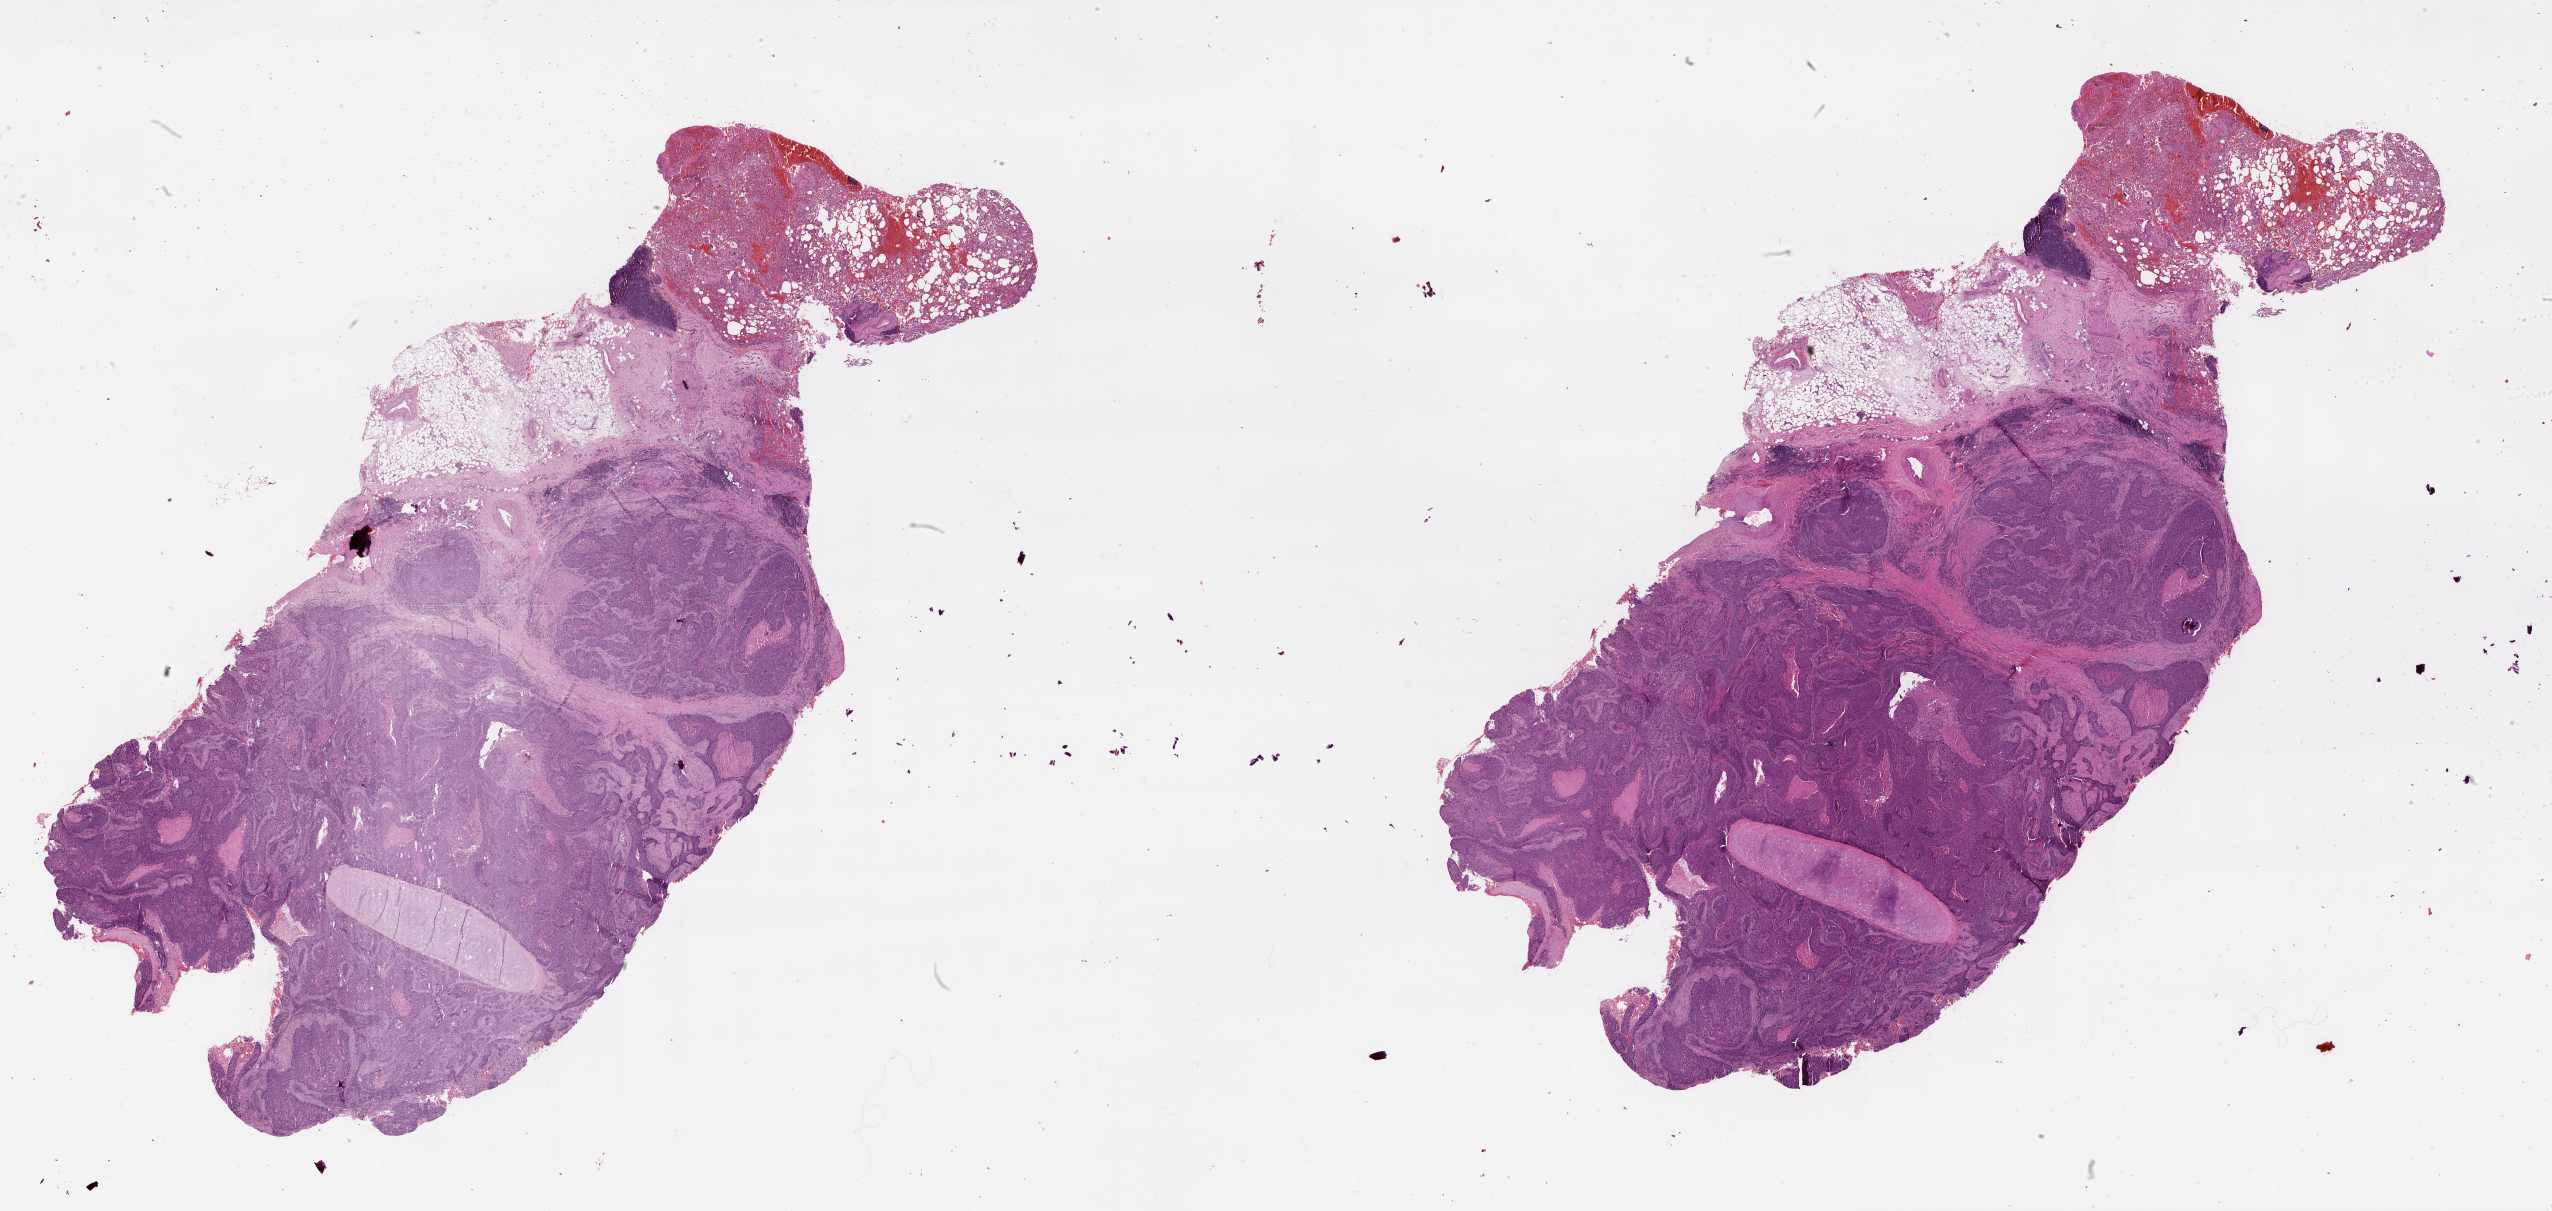
Whole-slide histology image, H&E — a low-resolution overview of the entire scanned area, about 41.1 x 19.5 mm (acquisition: 20x scan). Tumour tissue sample, lung. Patient: male, age 58 years.
Patient diagnosis (cohort enrolment): squamous cell carcinoma (lung).